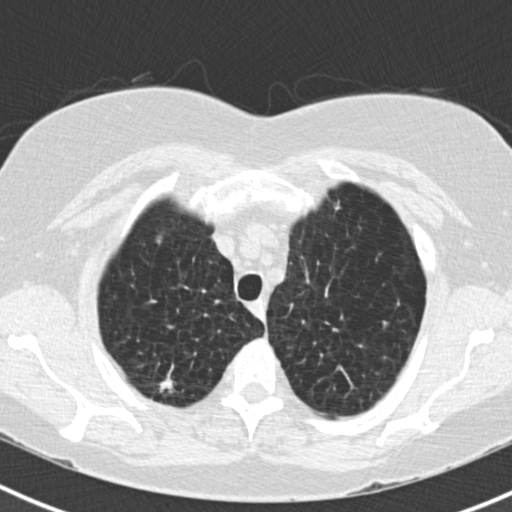
Low-dose screening chest CT, one axial slice. Slice 144 of 180 in the series (ordered by position). Reconstruction kernel B30f. Lung window (W 1500 / L -600 HU). 2 mm slice thickness. 512 × 512 image matrix.
Annotated regions visible in this slice (outlined manually by an expert reader):
- lesion 1 (tumor, upper lobe of right lung): bounding box <159,378,173,393> (left, top, right, bottom; pixels)